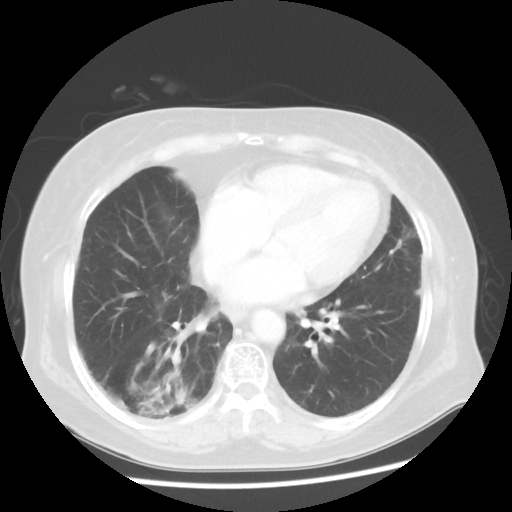
Chest CT, one axial slice; position 22 of 56 along the scan axis; 120 kVp; lung window (W 1500 / L -600 HU); 5 mm slice thickness; 512 × 512 image matrix, field of view 360 × 360 mm. Patient: female, 64 years. From the clinical record (not read from this slice): clinical TNM (as recorded): Tis N0 M0.
Outlined on this slice (bounding box drawn by a radiologist):
- lung tumour (recorded histology: adenocarcinoma): bounding box (x1, y1, x2, y2) in pixels: (127, 362, 201, 422)